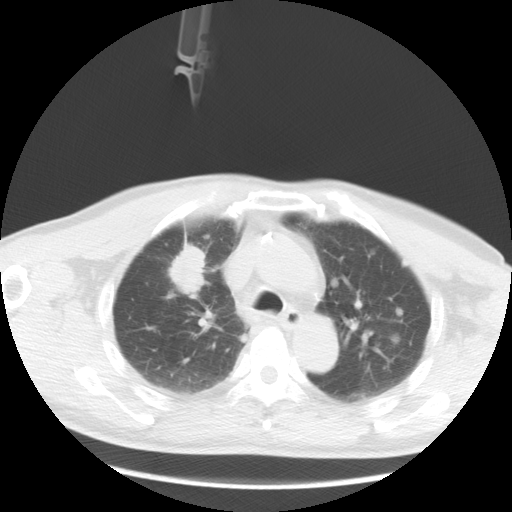
Chest CT, one axial slice. Position 21 of 35 along the scan axis. 120 kVp. Lung window (W 1500 / L -600 HU). 5 mm slice thickness. 512 × 512 image matrix, field of view 369 × 369 mm. Patient: male, 57 years. Case-level facts recorded for this patient, not image findings: clinical TNM (as recorded): T2 N3 M1a.
Annotated regions visible in this slice (rectangle marked by the reading radiologist):
- lung tumour (recorded histology: adenocarcinoma): box from (x=164, y=240) to (x=208, y=298) px